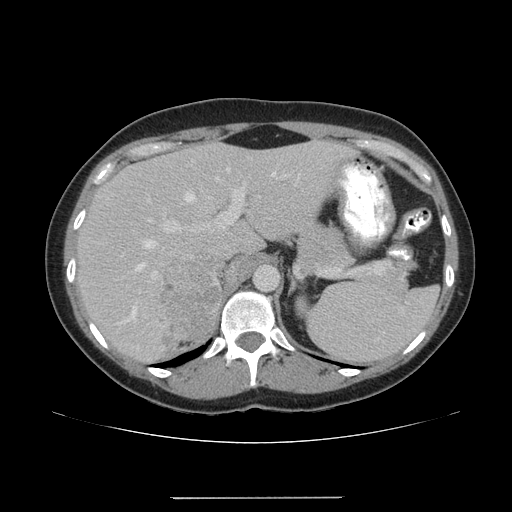
Contrast-enhanced abdominal CT, one axial slice; position 120 of 161 along the scan axis; 120 kVp; intravenous contrast given; soft-tissue window (W 400 / L 40 HU); 512 × 512 image matrix. Female patient. From the clinical record (not read from this slice): diagnosis: adrenocortical carcinoma; tumour side: right adrenal; tumour size at pathology: 9 cm; Ki-67 index: 14 %; stage (as recorded): 3.
Structures marked on this image (semi-automatically segmented with operator editing):
- mass: bounding box (x1, y1, x2, y2) in pixels: (159, 263, 221, 345)